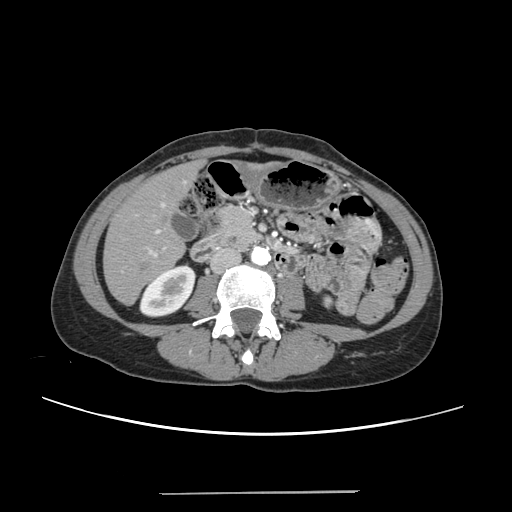
Contrast-enhanced abdominal CT, one axial slice. Slice 80 of 240 in the series (ordered by position). 120 kVp. Intravenous contrast given. Soft-tissue window (W 400 / L 40 HU). 1.25 mm slice thickness. 512 × 512 image matrix, field of view 371 × 371 mm. Female patient, age 60 years. Case-level facts recorded for this patient, not image findings: diagnosis: colorectal cancer liver metastases, imaged before liver resection; multiple liver metastases: no; largest metastasis: 1.5 cm; chemotherapy before resection: yes.
Structures marked on this image (expert manual segmentation):
- liver: bounding box <105,164,198,304> (left, top, right, bottom; pixels)
- planned liver remnant (the part of the liver to remain after resection): <105,172,184,304>
- portal vein (with intrahepatic branches): <136,203,165,257>